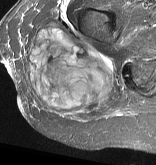
MRI of an extremity soft-tissue mass, one axial slice; slice 24 of 57 in the series (ordered by position); STIR; MR volume resampled by the dataset authors to the PET/CT grid (not the native acquisition matrix); 3.27 mm slice thickness; 156 × 165 image matrix. Female patient. Case-level facts recorded for this patient, not image findings: histological type: epithelioid sarcoma with vascular differentiation; site of the primary tumour: right buttock.
Outlined on this slice (expert contour drawn on MRI and transferred to this co-registered scan by the dataset authors):
- gross tumour volume (mass): box from (x=26, y=22) to (x=114, y=118) px